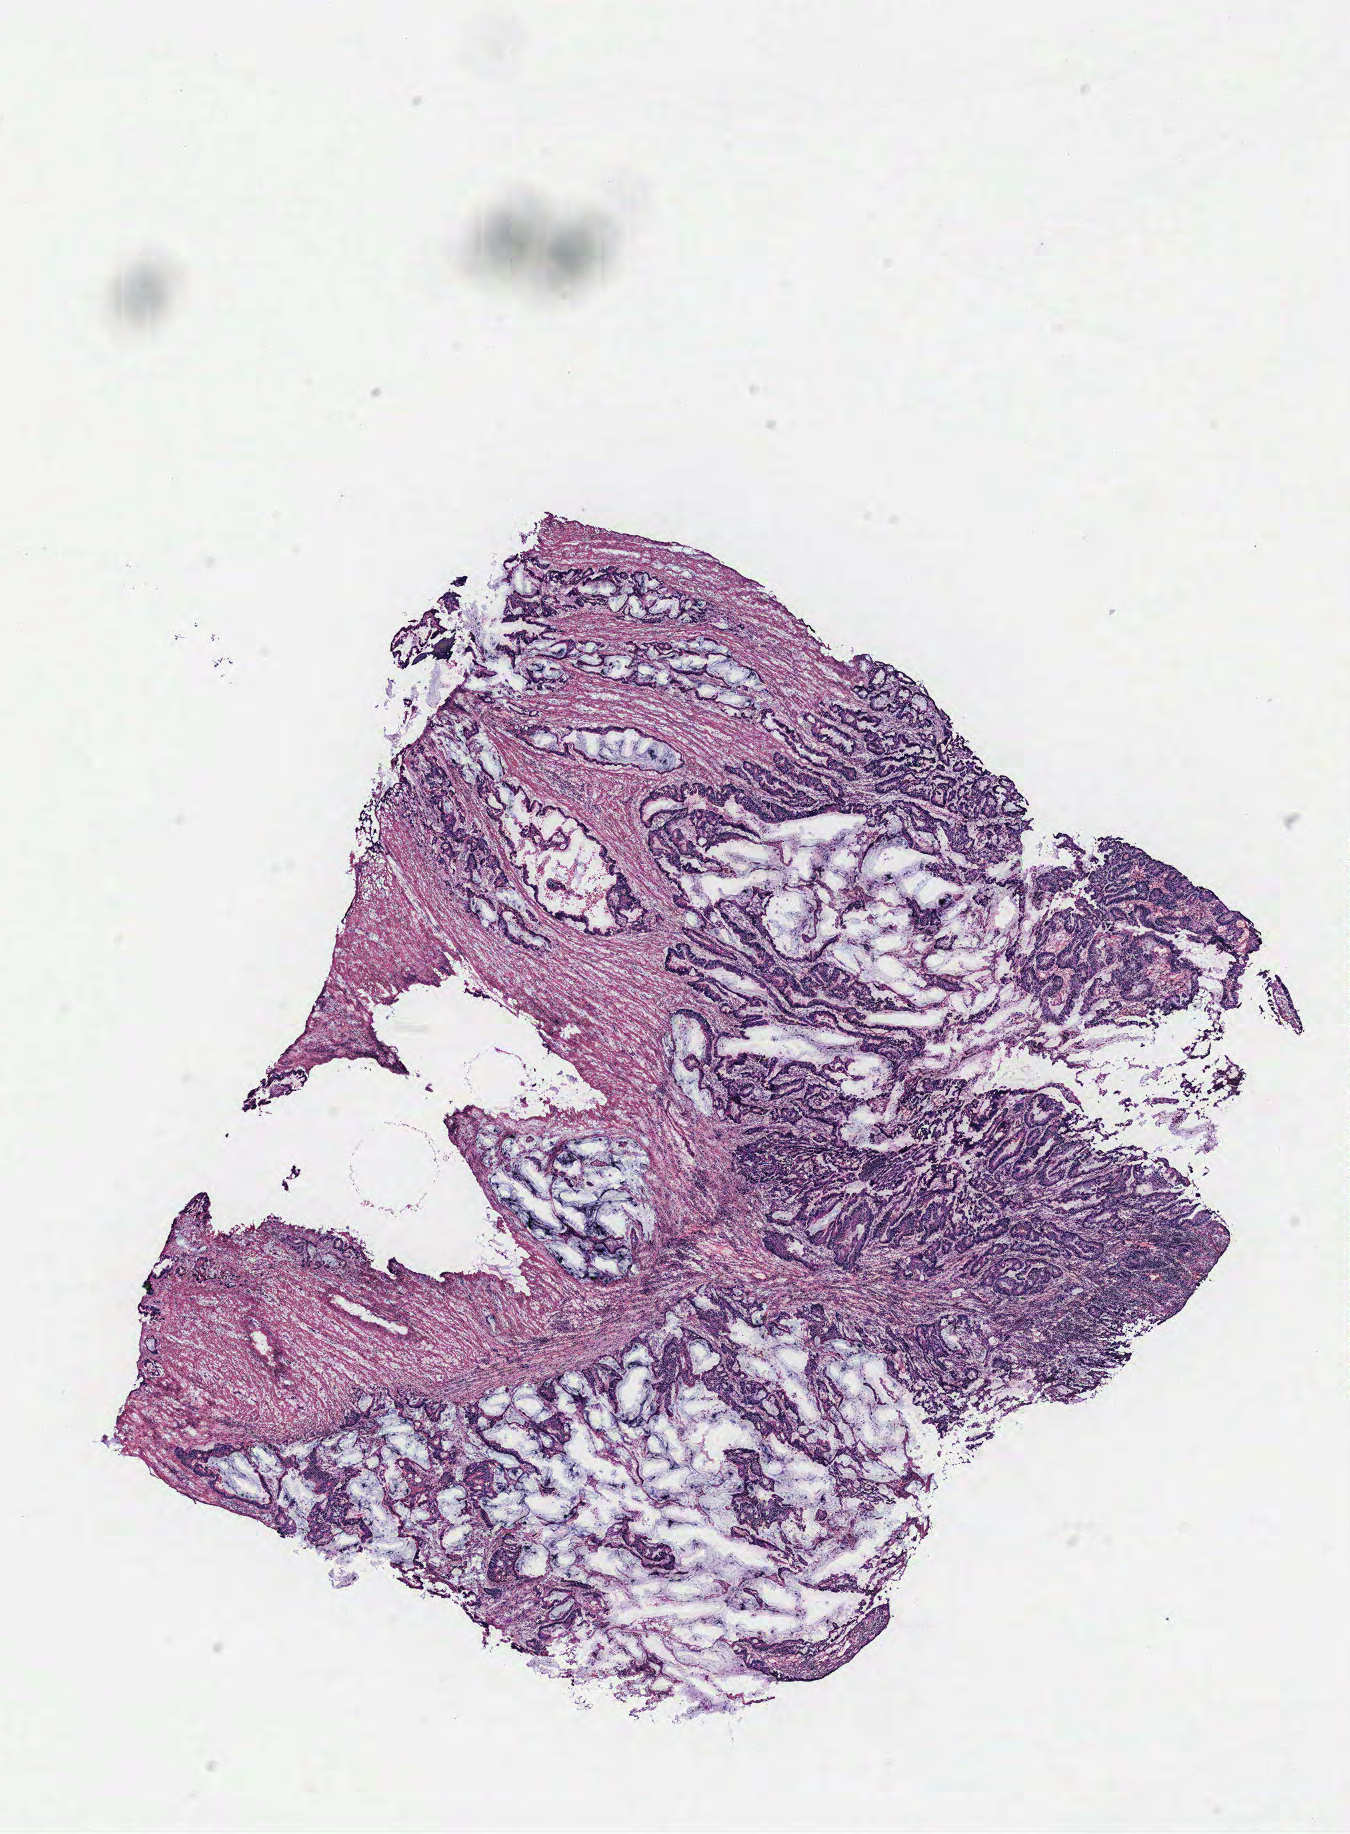
Whole-slide histology image, H&E-stained, a low-resolution overview of the entire scanned area, about 10.8 x 14.7 mm (from a 40x scan), tumour tissue sample, colon. Male, 70 y/o.
Primary tumour site (as recorded): colon. Patient diagnosis (cohort enrolment): colon cancer (colon).